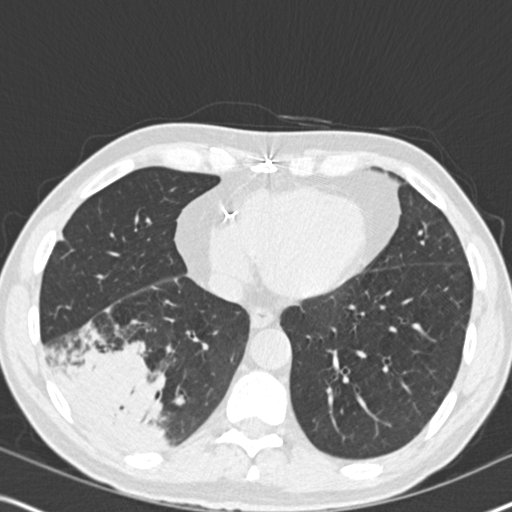
Axial slice from a low-dose chest CT screening exam, second screening round (one year after baseline), lung window (W 1500 / L -600 HU), 2 mm slice thickness, slice 115 of 182 in the series, 512 × 512 image matrix. Male, age 61 years at enrolment. Current smoker at enrolment.
Expert-annotated lung lesion, bounding box <41,312,187,461> (left, top, right, bottom; pixels). Reader record for this screening exam (exam-level; its link to the box is not recorded): non-calcified nodule or mass ≥4 mm, right lower lobe, 90 × 80 mm, soft tissue attenuation, pre-existing on the prior screen: yes; interval growth: yes. Lung cancer was diagnosed 20 days after this screen: bronchiolo-alveolar adenocarcinoma, NOS, right lower lobe, moderately differentiated (G2), stage IIIB (AJCC 6th edition), 90 mm at pathology.